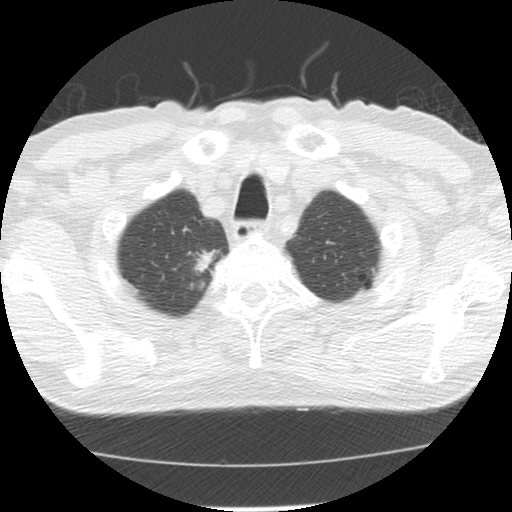
Axial slice from a low-dose chest CT screening exam, baseline screening round, lung window (W 1500 / L -600 HU), standard (soft-tissue) reconstruction kernel (STANDARD), slice 21 of 139 in the series. Male participant, aged 64 years at enrolment. Former smoker at enrolment.
- Expert-annotated lung lesion, bounding box [x1, y1, x2, y2] px = [181, 242, 225, 282].
- Screening reader's record for this exam (one nodule recorded; not confirmed to be the boxed lesion): non-calcified nodule or mass ≥4 mm, right upper lobe, 20 × 13 mm, spiculated (stellate) margins, soft tissue attenuation.
- Later outcome: lung cancer diagnosed 73 days after this screen — adenocarcinoma, NOS, right upper lobe, moderately differentiated (G2), stage IA (AJCC 6th edition), 17 mm at pathology.